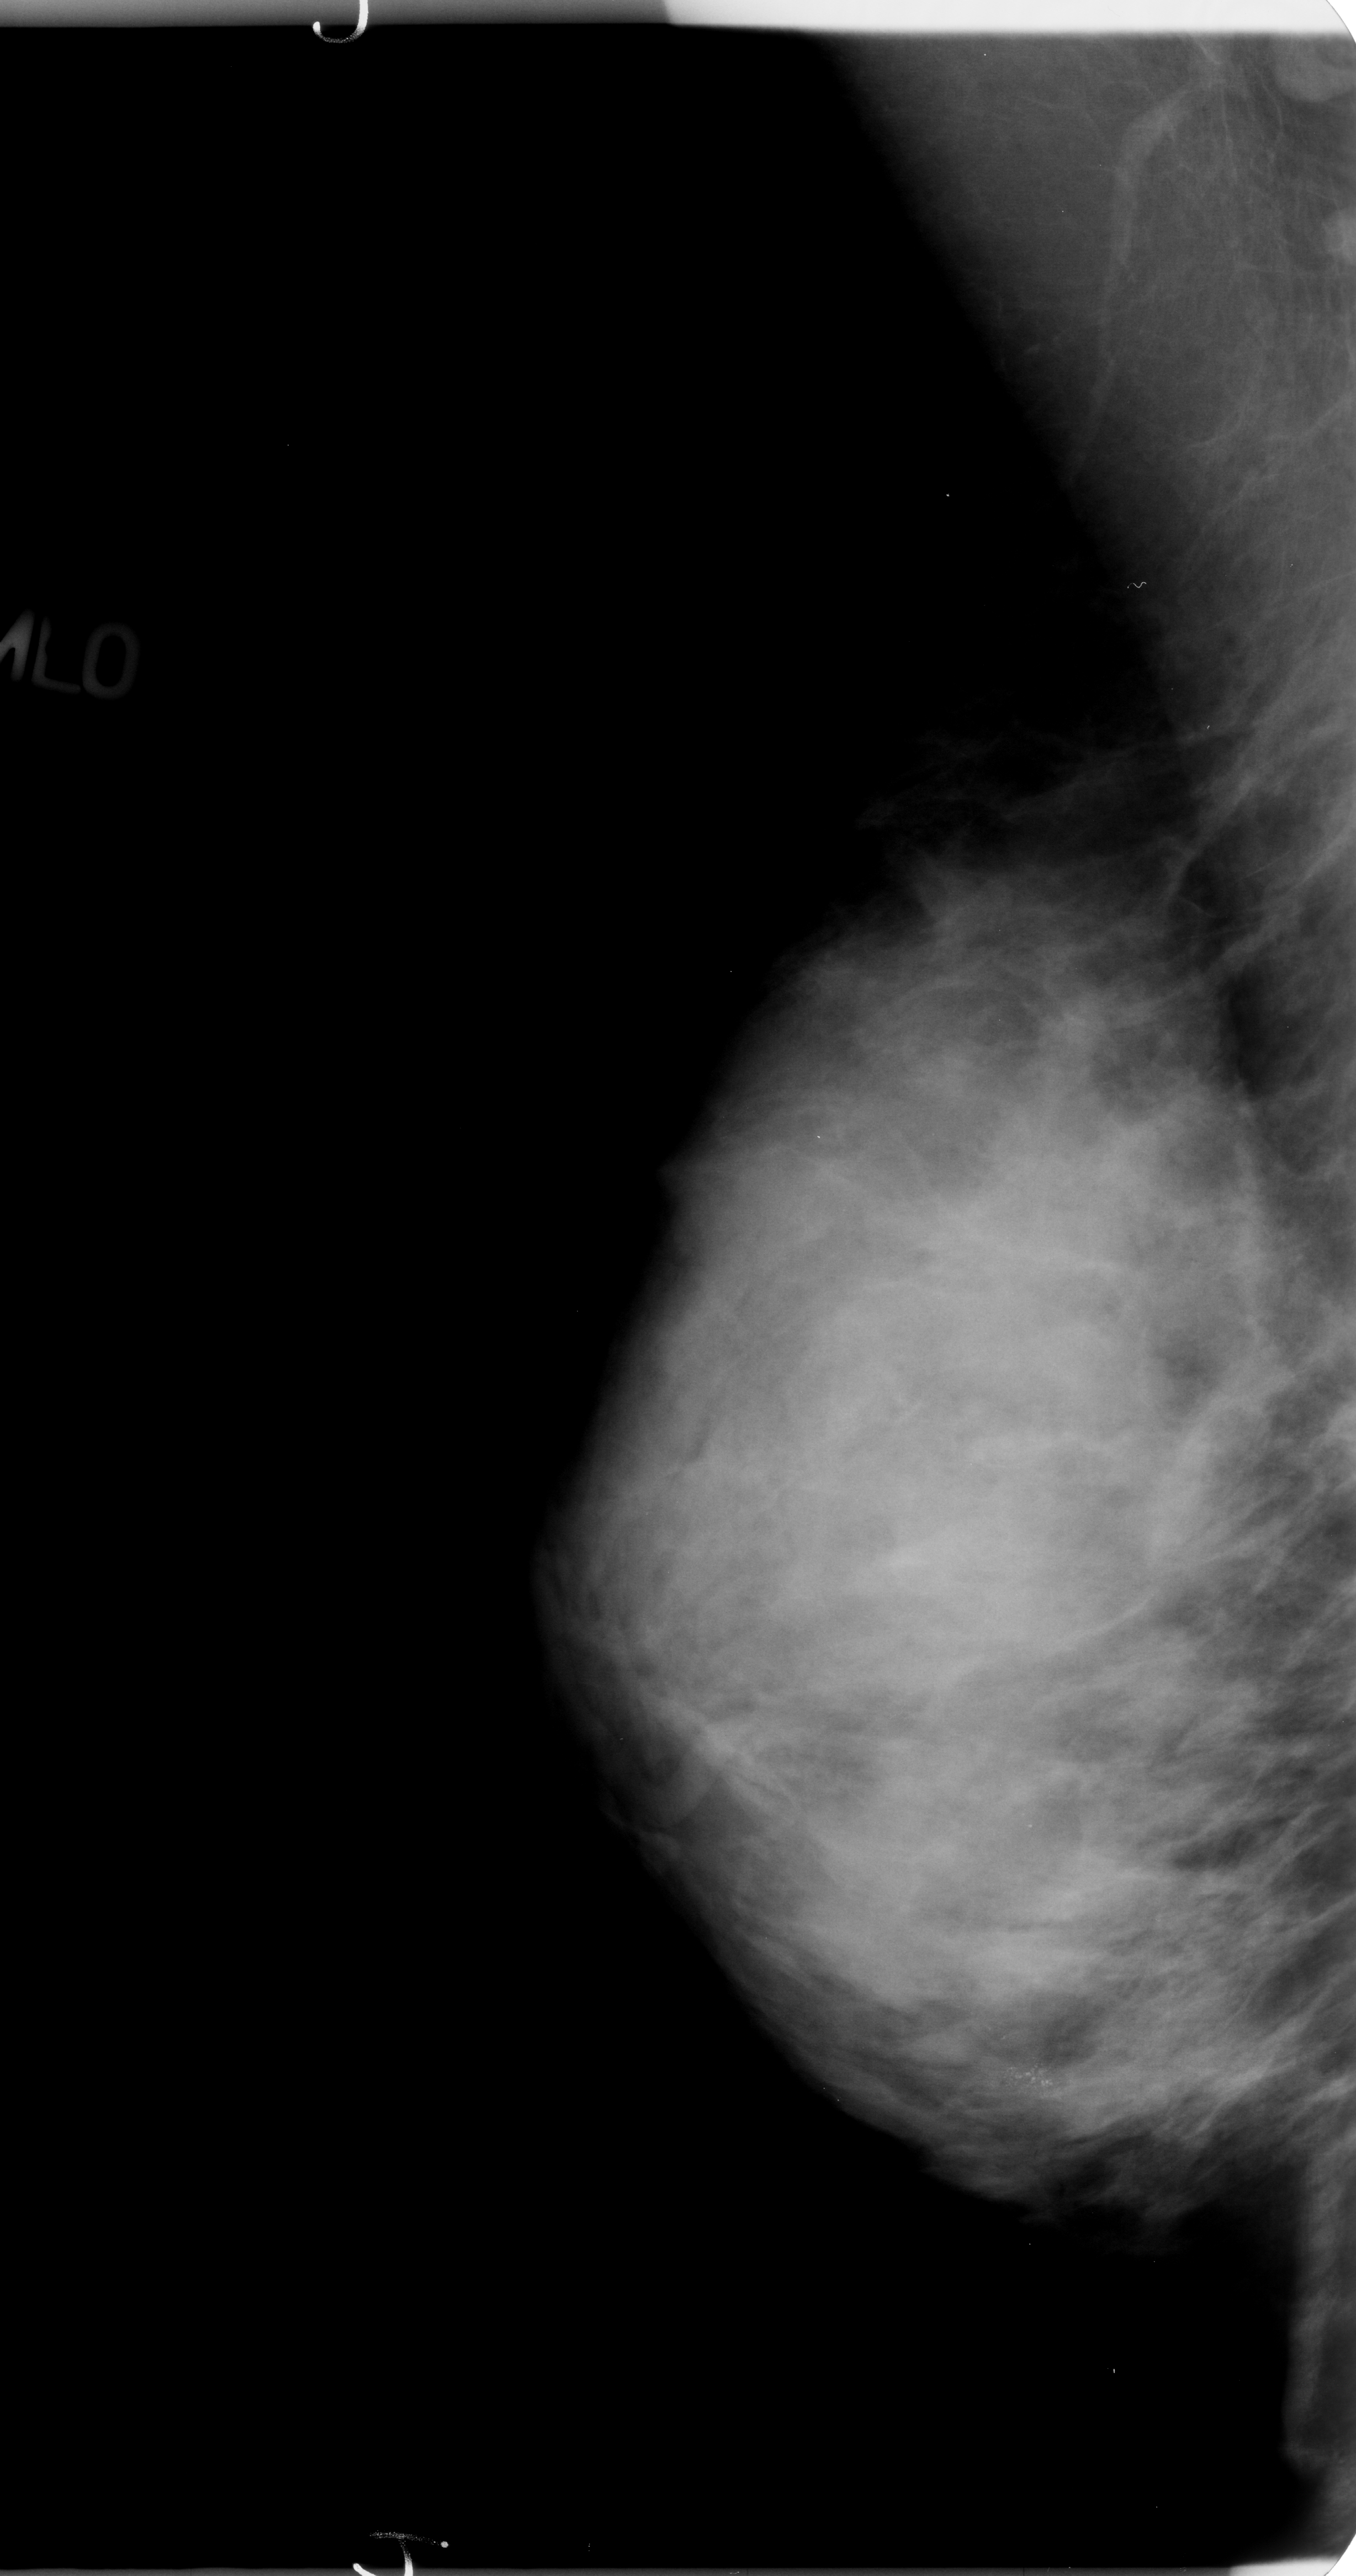
Mammogram (digitized film). Right breast. Mediolateral oblique (MLO) view. Breast composition: extremely dense (BI-RADS density category 4 of 4). 1356 × 2576 image matrix.
Marked abnormalities (boxes around the expert regions of interest):
- calcifications, morphology pleomorphic, distribution clustered; BI-RADS assessment category 4; pathology result (as recorded, not read from the image): benign: box from (x=980, y=2014) to (x=1079, y=2131) px